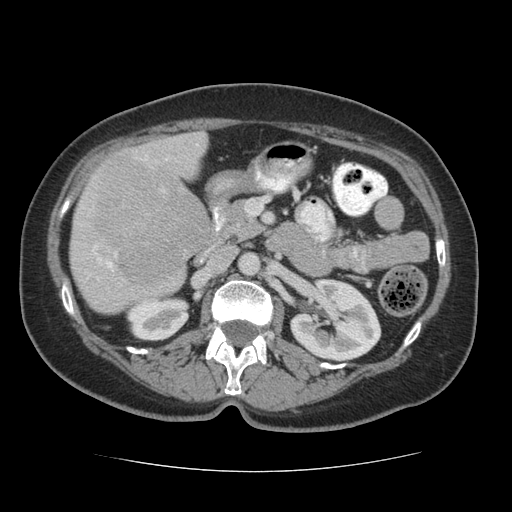
Contrast-enhanced abdominal CT (liver protocol), one axial slice. Position 22 of 75 along the scan axis. 140 kVp. Soft-tissue window (W 400 / L 40 HU). 2.5 mm slice thickness. 512 × 512 image matrix, field of view 360 × 360 mm. From the clinical record (not read from this slice): diagnosis: hepatocellular carcinoma (patient treated with transarterial chemoembolisation; whether this scan precedes or follows treatment is not stated here); TNM stage (as recorded): Stage-I; Child-Pugh class: A; tumour differentiation: moderately differentiated; tumour nodularity: uninodular.
Outlined on this slice (semi-automatic segmentation, software-assisted and operator-edited):
- liver parenchyma outside the tumour (the mass and vessels are separate outlines, so this box may not span the whole liver): box from (x=70, y=132) to (x=210, y=314) px
- mass: (x=83, y=154)–(x=209, y=291)
- liver vessels: (x=97, y=144)–(x=198, y=279)